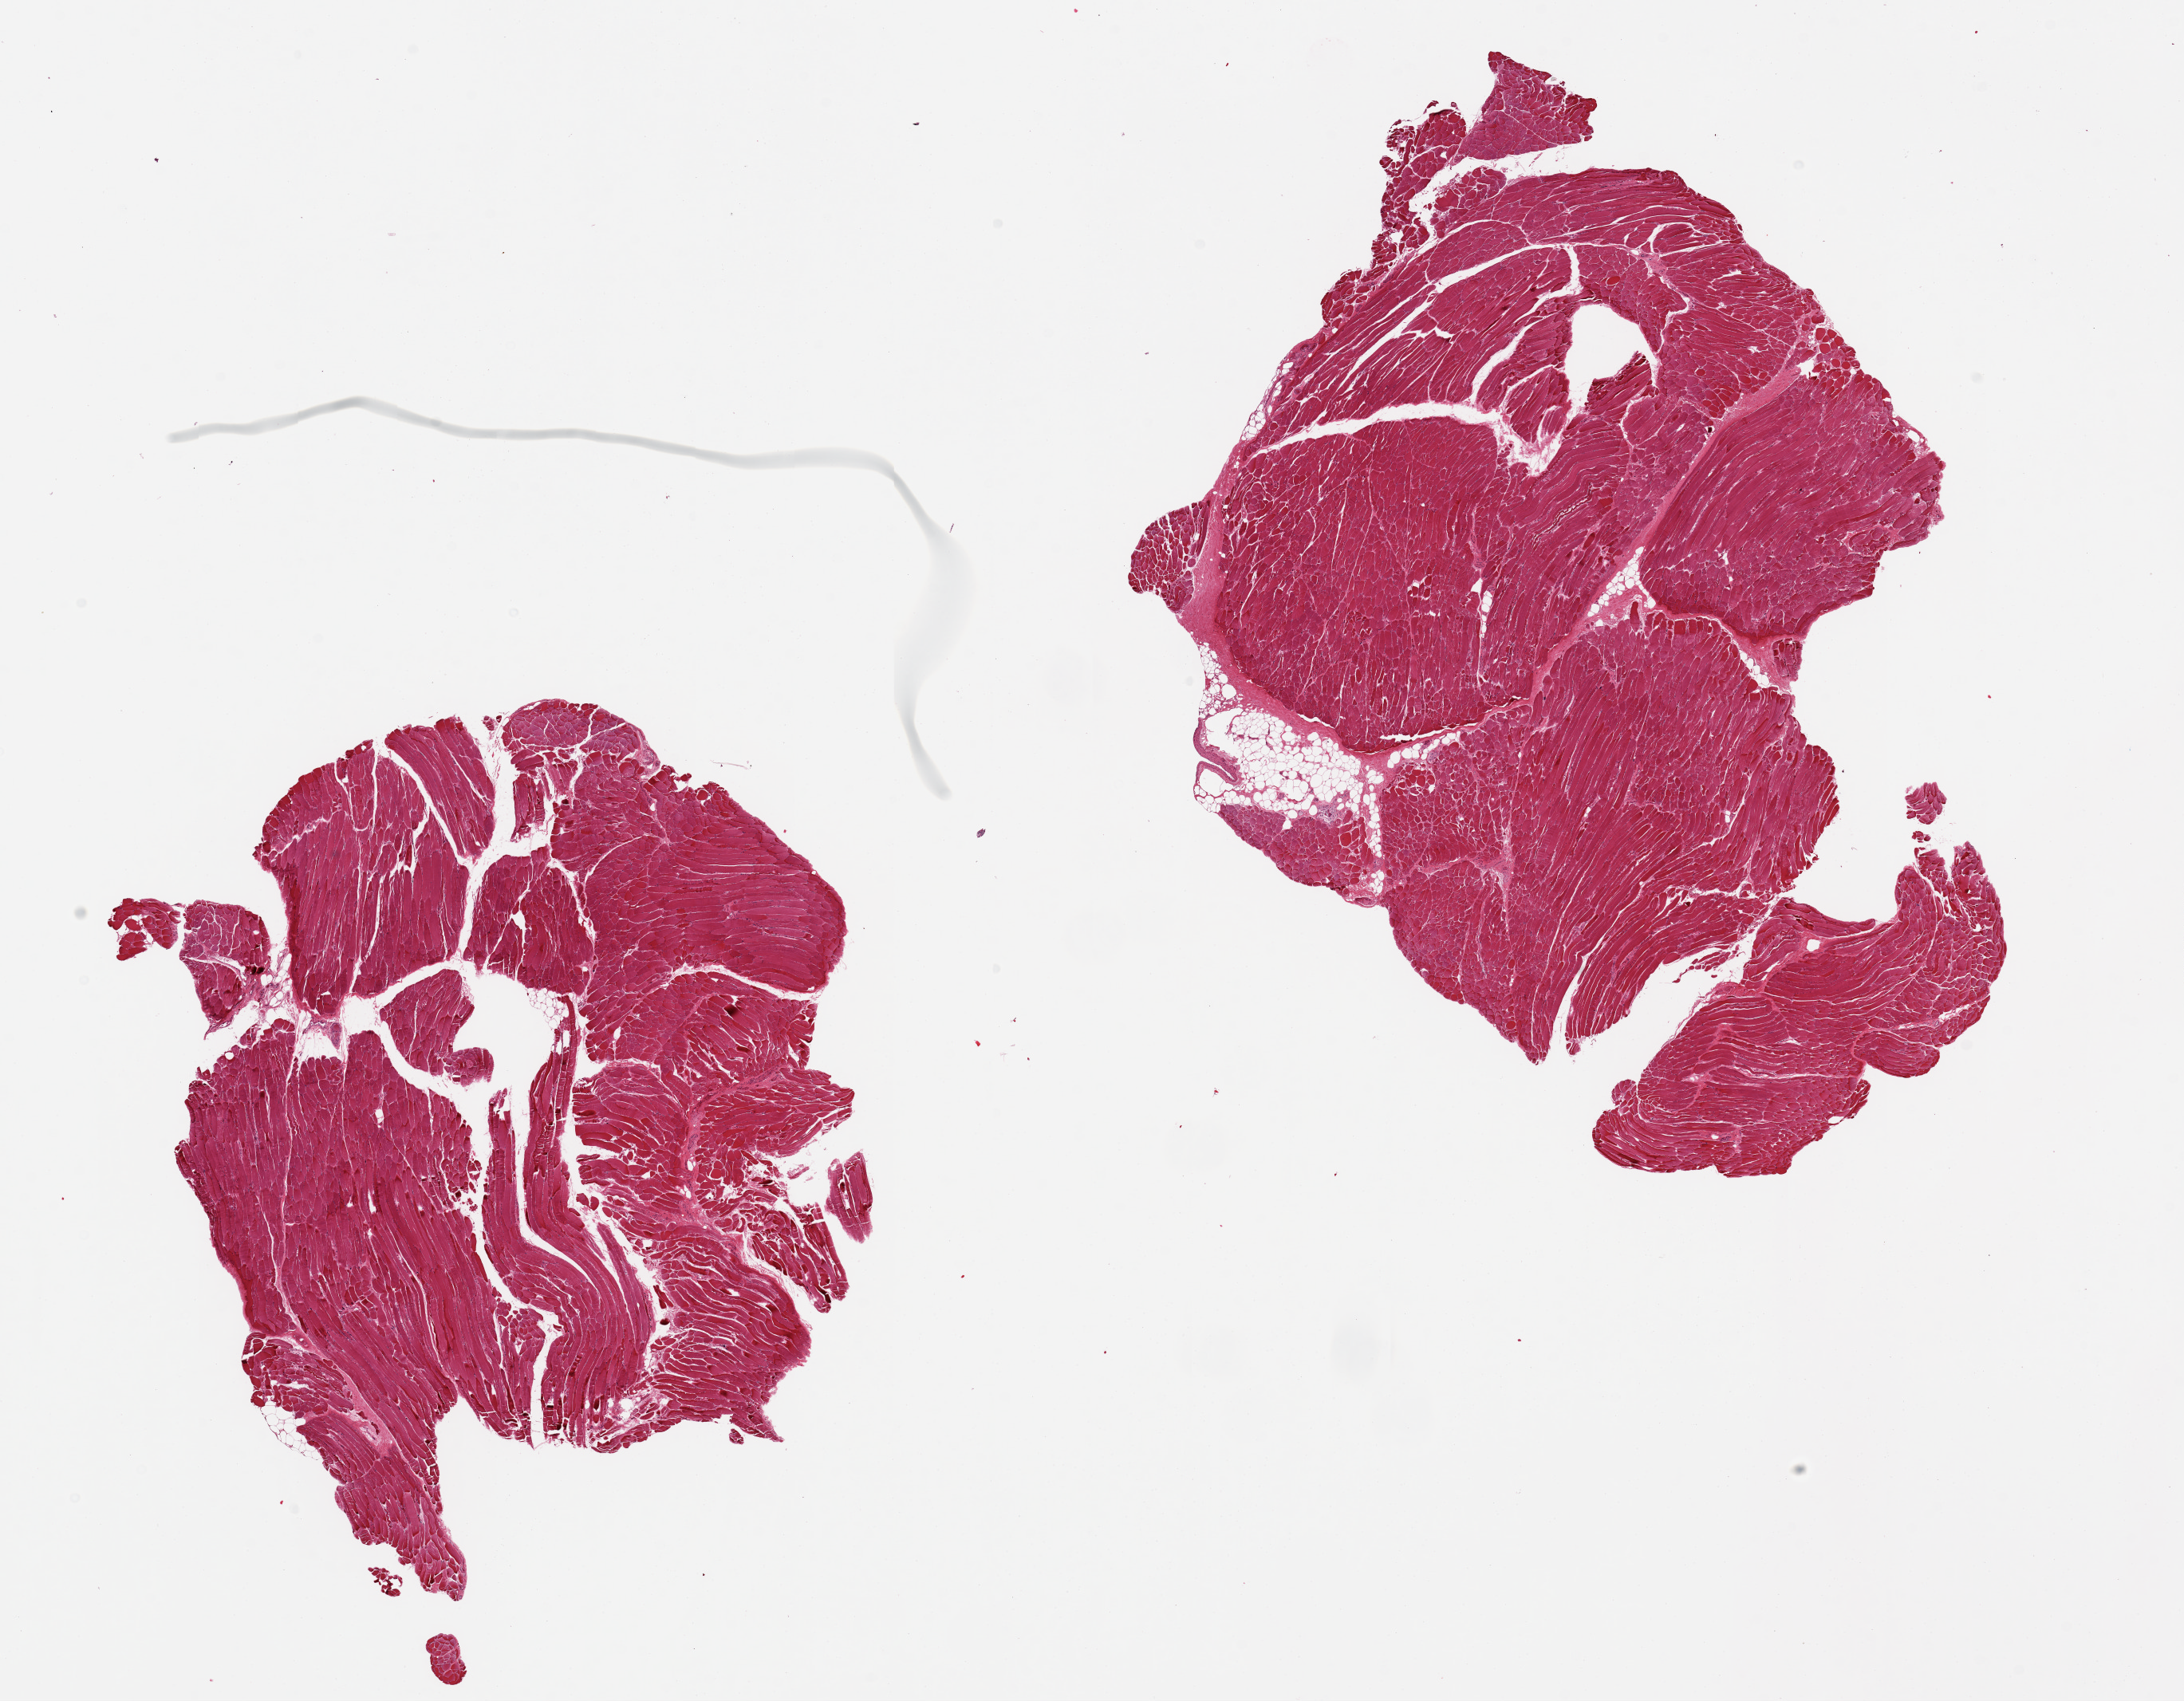
Hematoxylin and eosin (H&E) whole-slide image — shown as a low-resolution overview of the whole scanned area (about 21.7 x 16.9 mm, from a 20x scan). PAXgene-fixed, paraffin-embedded tissue. Target tissue: skeletal muscle. Donor tissue sample. Male donor.
Reviewer comment on this tissue sample: 2 pieces, ~5% interstitial fat.